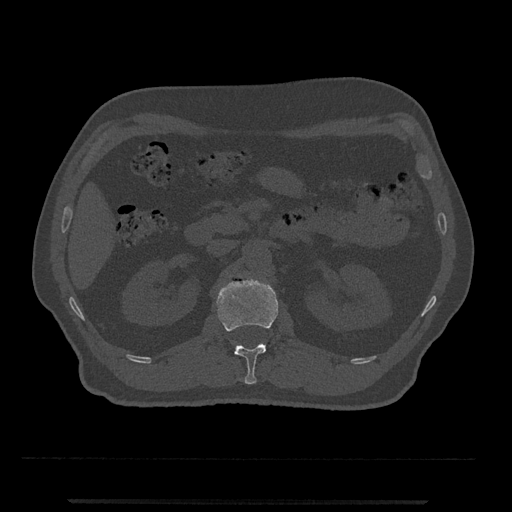
CT including the spine, one axial slice; position 320 of 797 along the scan axis; reconstruction kernel Br40s/3; 120 kVp; bone window (W 1800 / L 400 HU); 512 × 512 image matrix, field of view 419 × 419 mm. Patient: male, 63 years. Case-level facts recorded for this patient, not image findings: primary cancer: prostate.
Annotated regions visible in this slice (semi-automatic segmentation, software-assisted and operator-edited):
- L1 vertebra: bounding box <217,278,278,385> (left, top, right, bottom; pixels)